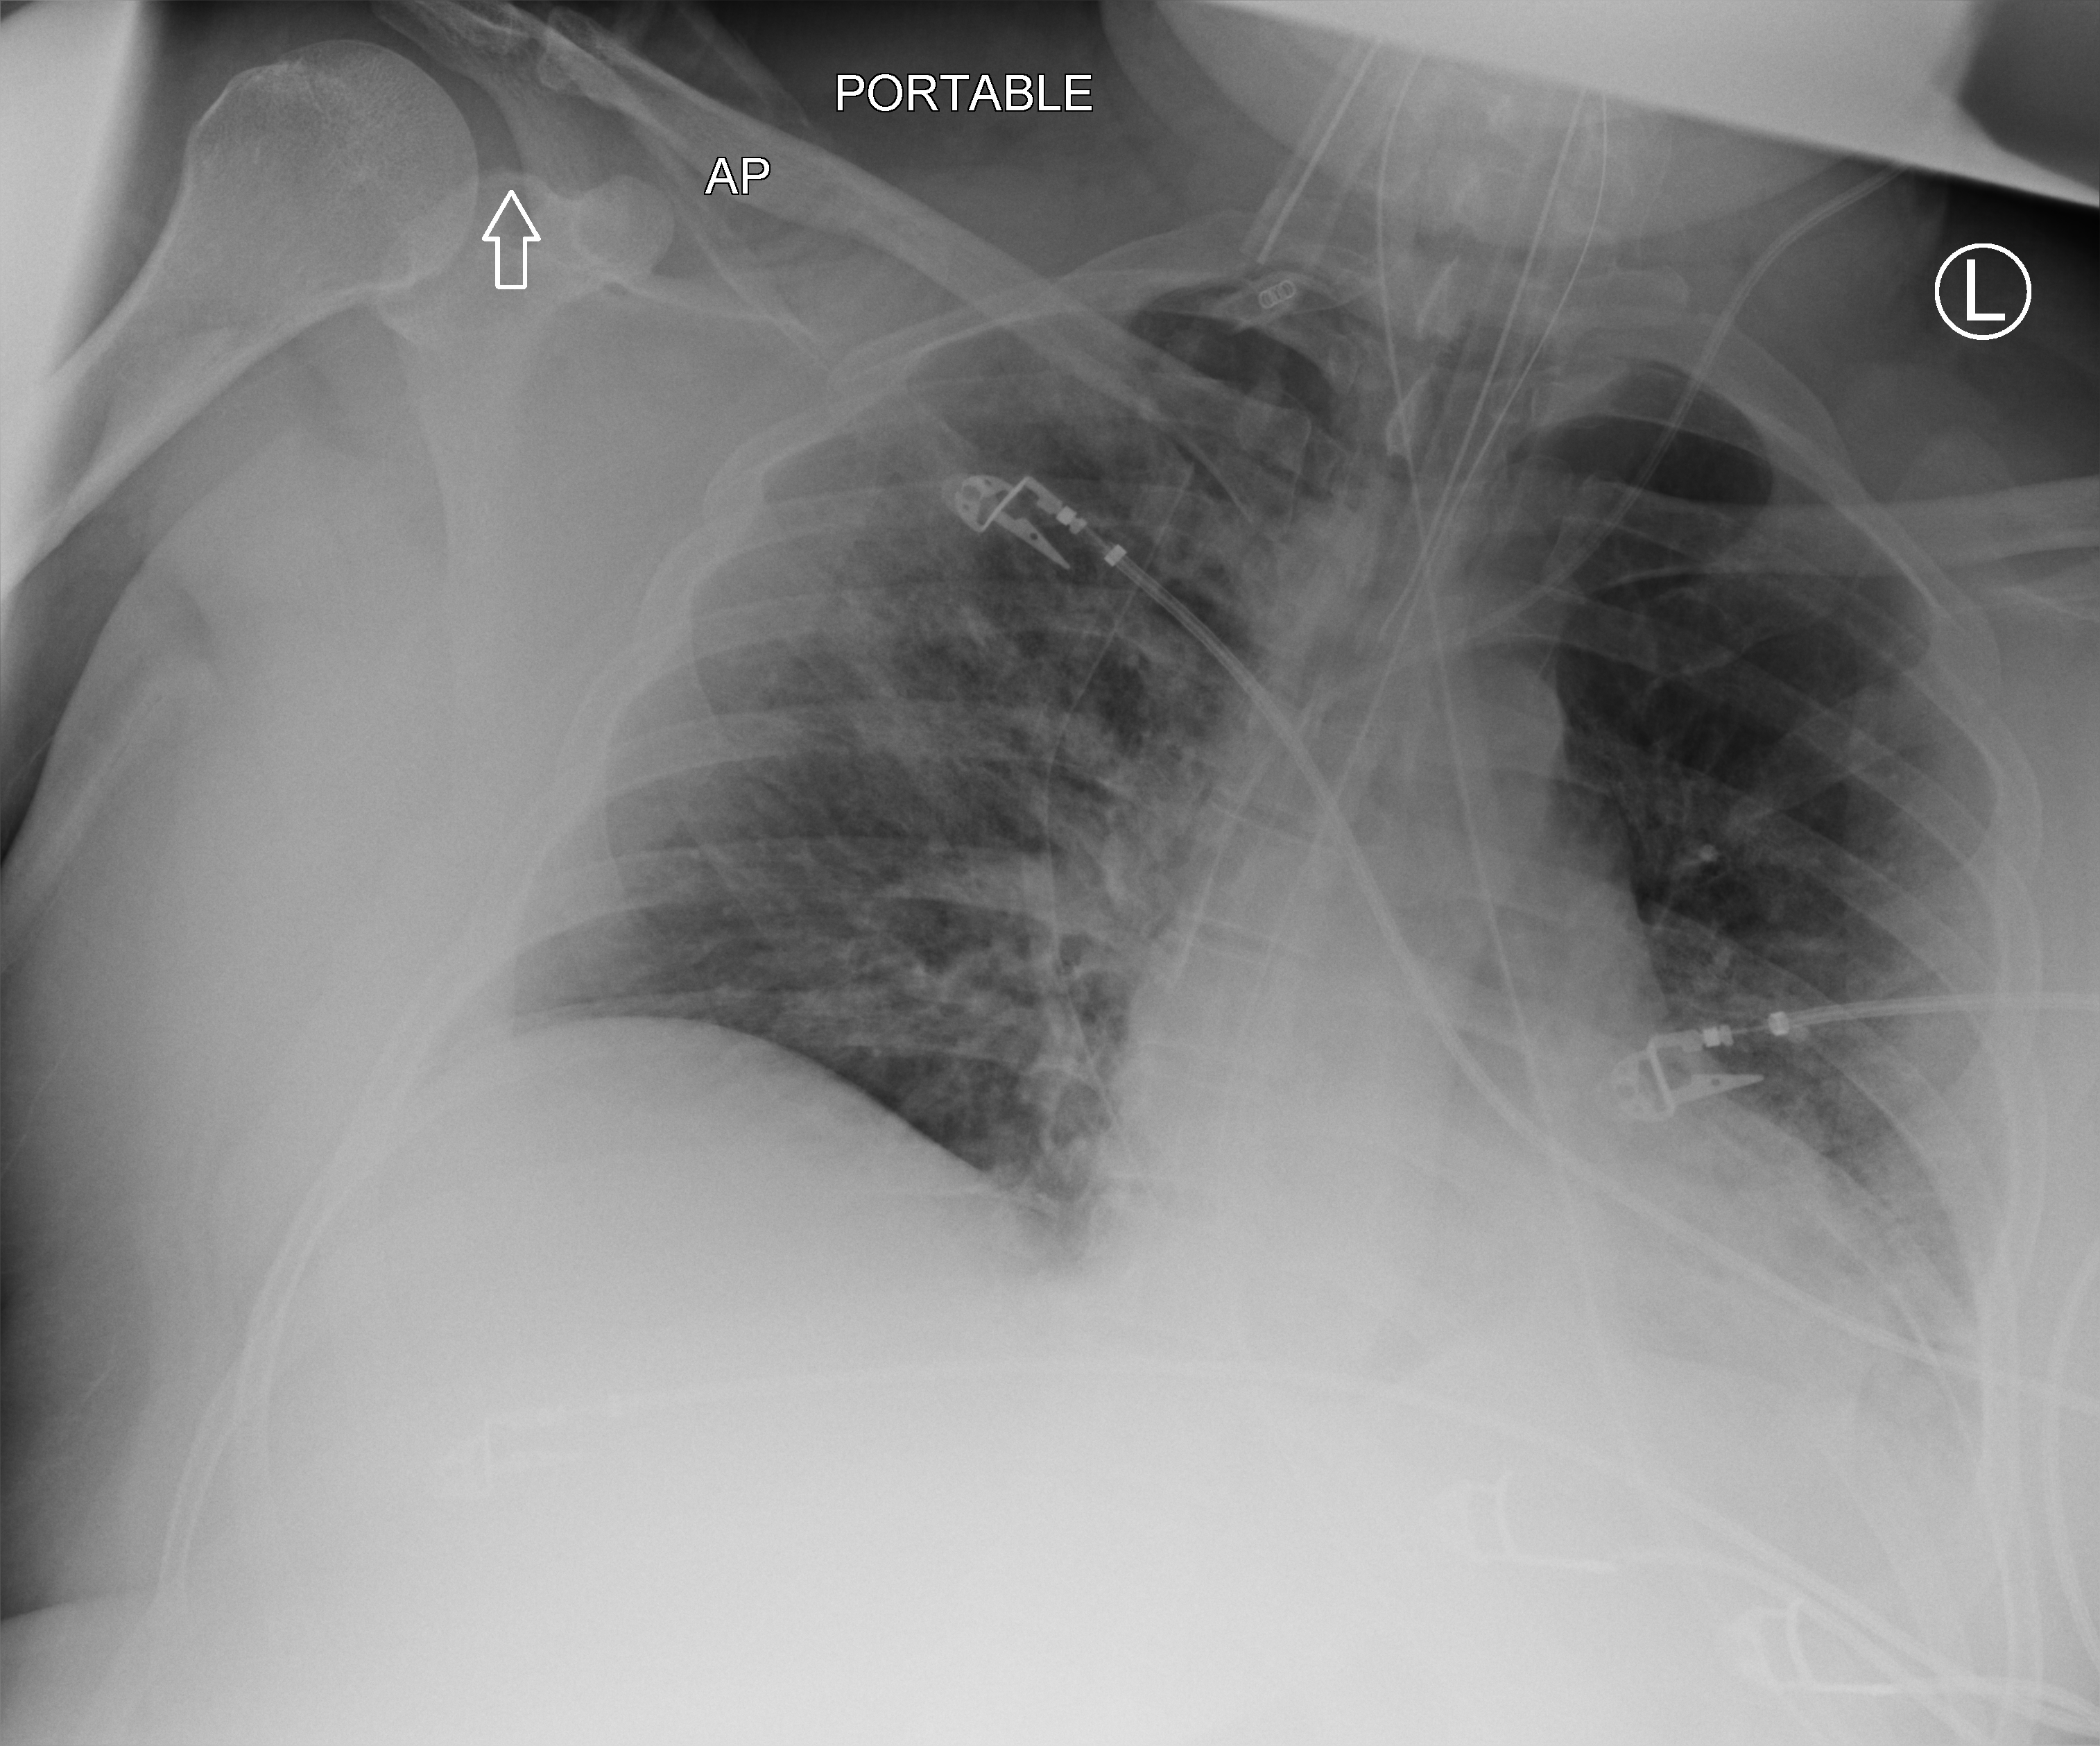
Chest X-ray (portable); anteroposterior (AP) projection. Adult patient hospitalised with COVID-19, age 18–59 years.
Hospital-stay facts (about this admission, not read from this image; timing relative to this image not recorded): length of hospital stay: 16 days; admitted to intensive care during this hospital stay: yes.